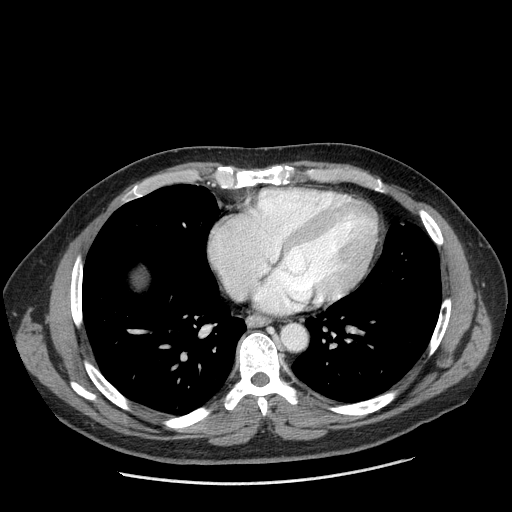
Contrast-enhanced abdominal CT (liver protocol), one axial slice. Position 189 of 198 along the scan axis. Reconstruction kernel STANDARD. 120 kVp. One of 2 acquisitions stored at this slice position. Soft-tissue window (W 400 / L 40 HU). 2.5 mm slice thickness. 512 × 512 image matrix, field of view 400 × 400 mm. Case-level facts recorded for this patient, not image findings: diagnosis: hepatocellular carcinoma (patient treated with transarterial chemoembolisation; whether this scan precedes or follows treatment is not stated here); TNM stage (as recorded): Stage-II; Child-Pugh class: A; tumour differentiation: moderately differentiated.
Annotated regions visible in this slice (semi-automatically segmented with operator editing):
- liver parenchyma outside the tumour (the mass and vessels are separate outlines, so this box may not span the whole liver): bounding box <132,270,146,286> (left, top, right, bottom; pixels)